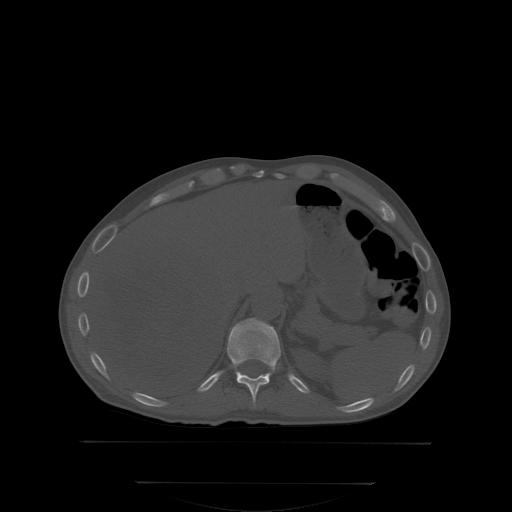
CT including the spine, one axial slice. Position 179 of 350 along the scan axis. Bone window (W 1800 / L 400 HU). 2.5 mm slice thickness. 512 × 512 image matrix, field of view 500 × 500 mm. Patient: male, 58 years. Case-level facts recorded for this patient, not image findings: primary cancer: prostate.
Annotated regions visible in this slice (semi-automatically segmented with operator editing):
- T11 vertebra: box from (x=228, y=320) to (x=280, y=405) px